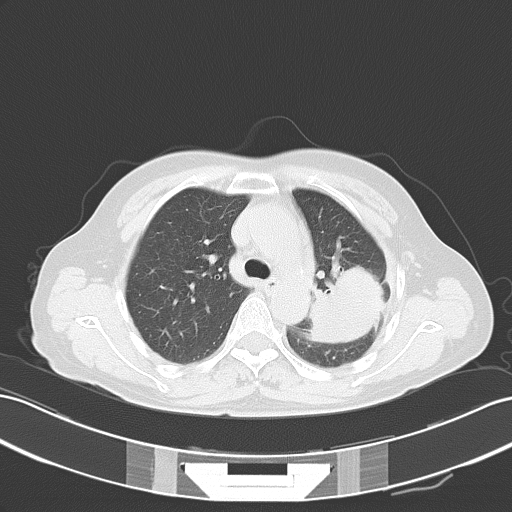
Chest CT, one axial slice. Slice 35 of 51 in the series (ordered by position). Lung window (W 1500 / L -600 HU). 512 × 512 image matrix, field of view 353 × 353 mm. Patient: female, 54 years. Case-level facts recorded for this patient, not image findings: clinical TNM (as recorded): T3 N1 M0.
Outlined on this slice (bounding box drawn by a radiologist):
- lung tumour (recorded histology: adenocarcinoma): bounding box [x1, y1, x2, y2] px = [309, 259, 382, 353]